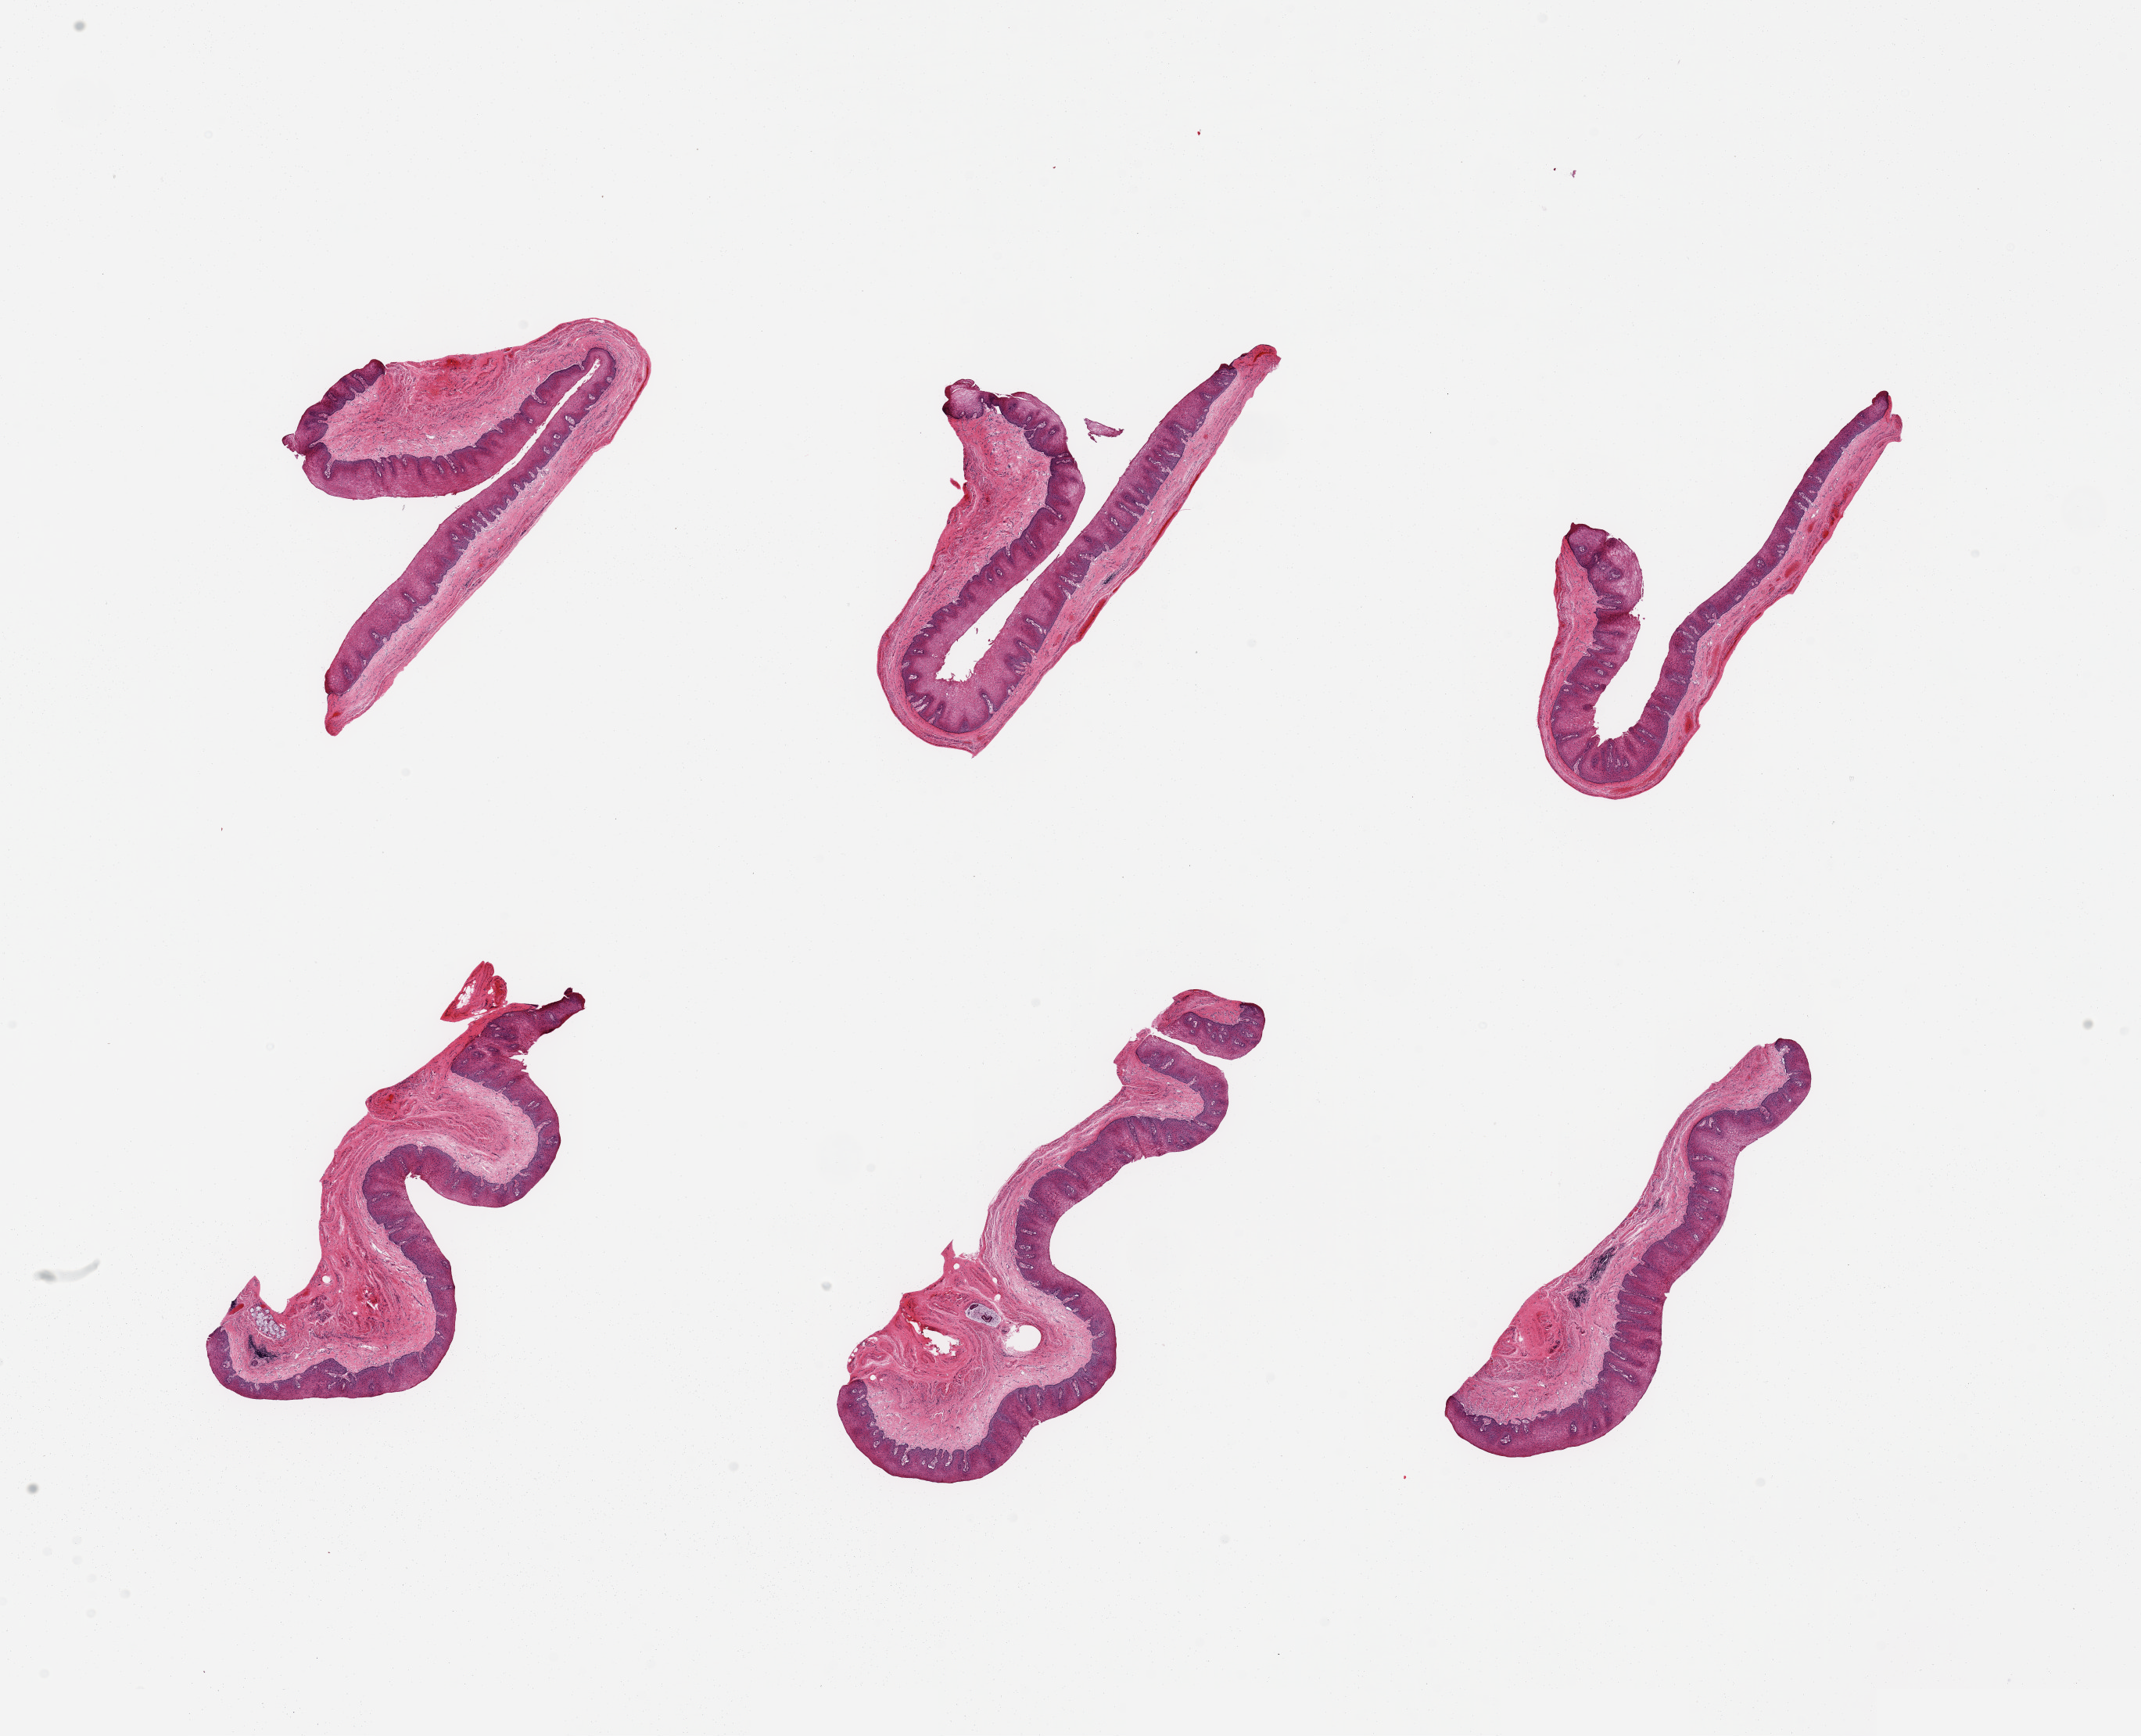
Digitized haematoxylin and eosin-stained section — a low-resolution overview of the entire scanned area, about 21.7 x 17.6 mm (slide scanned at 20x). PAXgene-fixed, paraffin-embedded tissue. Target tissue: esophageal mucous membrane. Donor tissue sample. Donor: male.
* pathologist's review note for this sample: 6 pieces, sqaumous mucosa up to ~0.4mm, ~40-50% of thickness